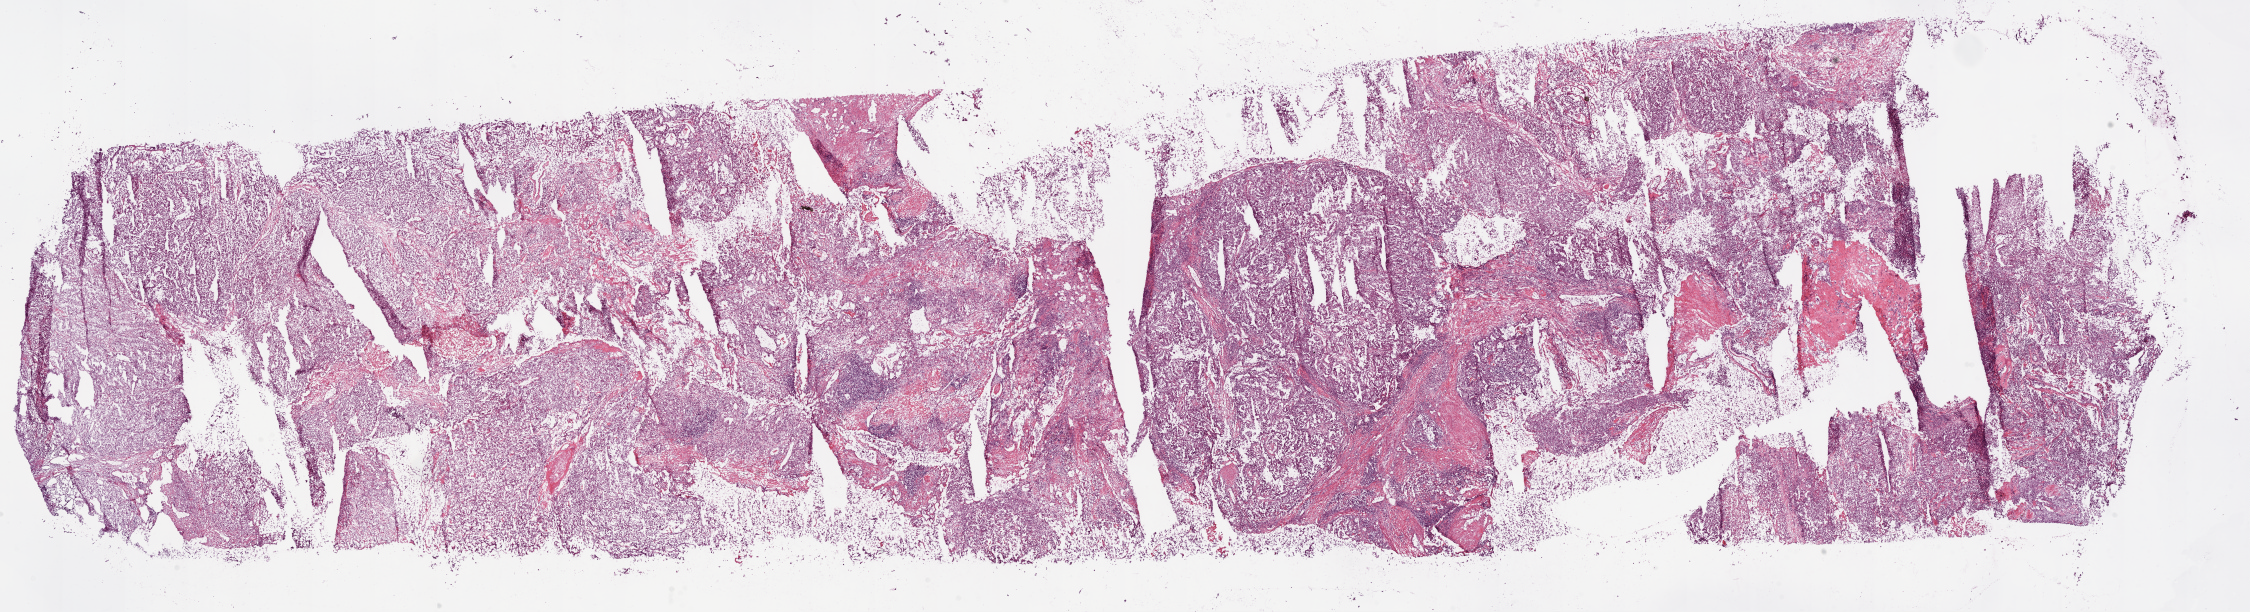
H&E whole-slide image — a low-resolution overview of the entire scanned area, about 36.1 x 9.8 mm. Frozen section from the bottom of the tissue portion. Sample: primary tumour, kidney. Male, age 57 years at initial diagnosis. Histologic grade: G3 (poorly differentiated). Slide review estimates, as recorded: tumour cells 80%, tumour nuclei 75%, normal cells 0%, stromal cells 20%, necrosis 0%.
* AJCC pathologic stage: III
* pathologic diagnosis: Clear cell adenocarcinoma, NOS